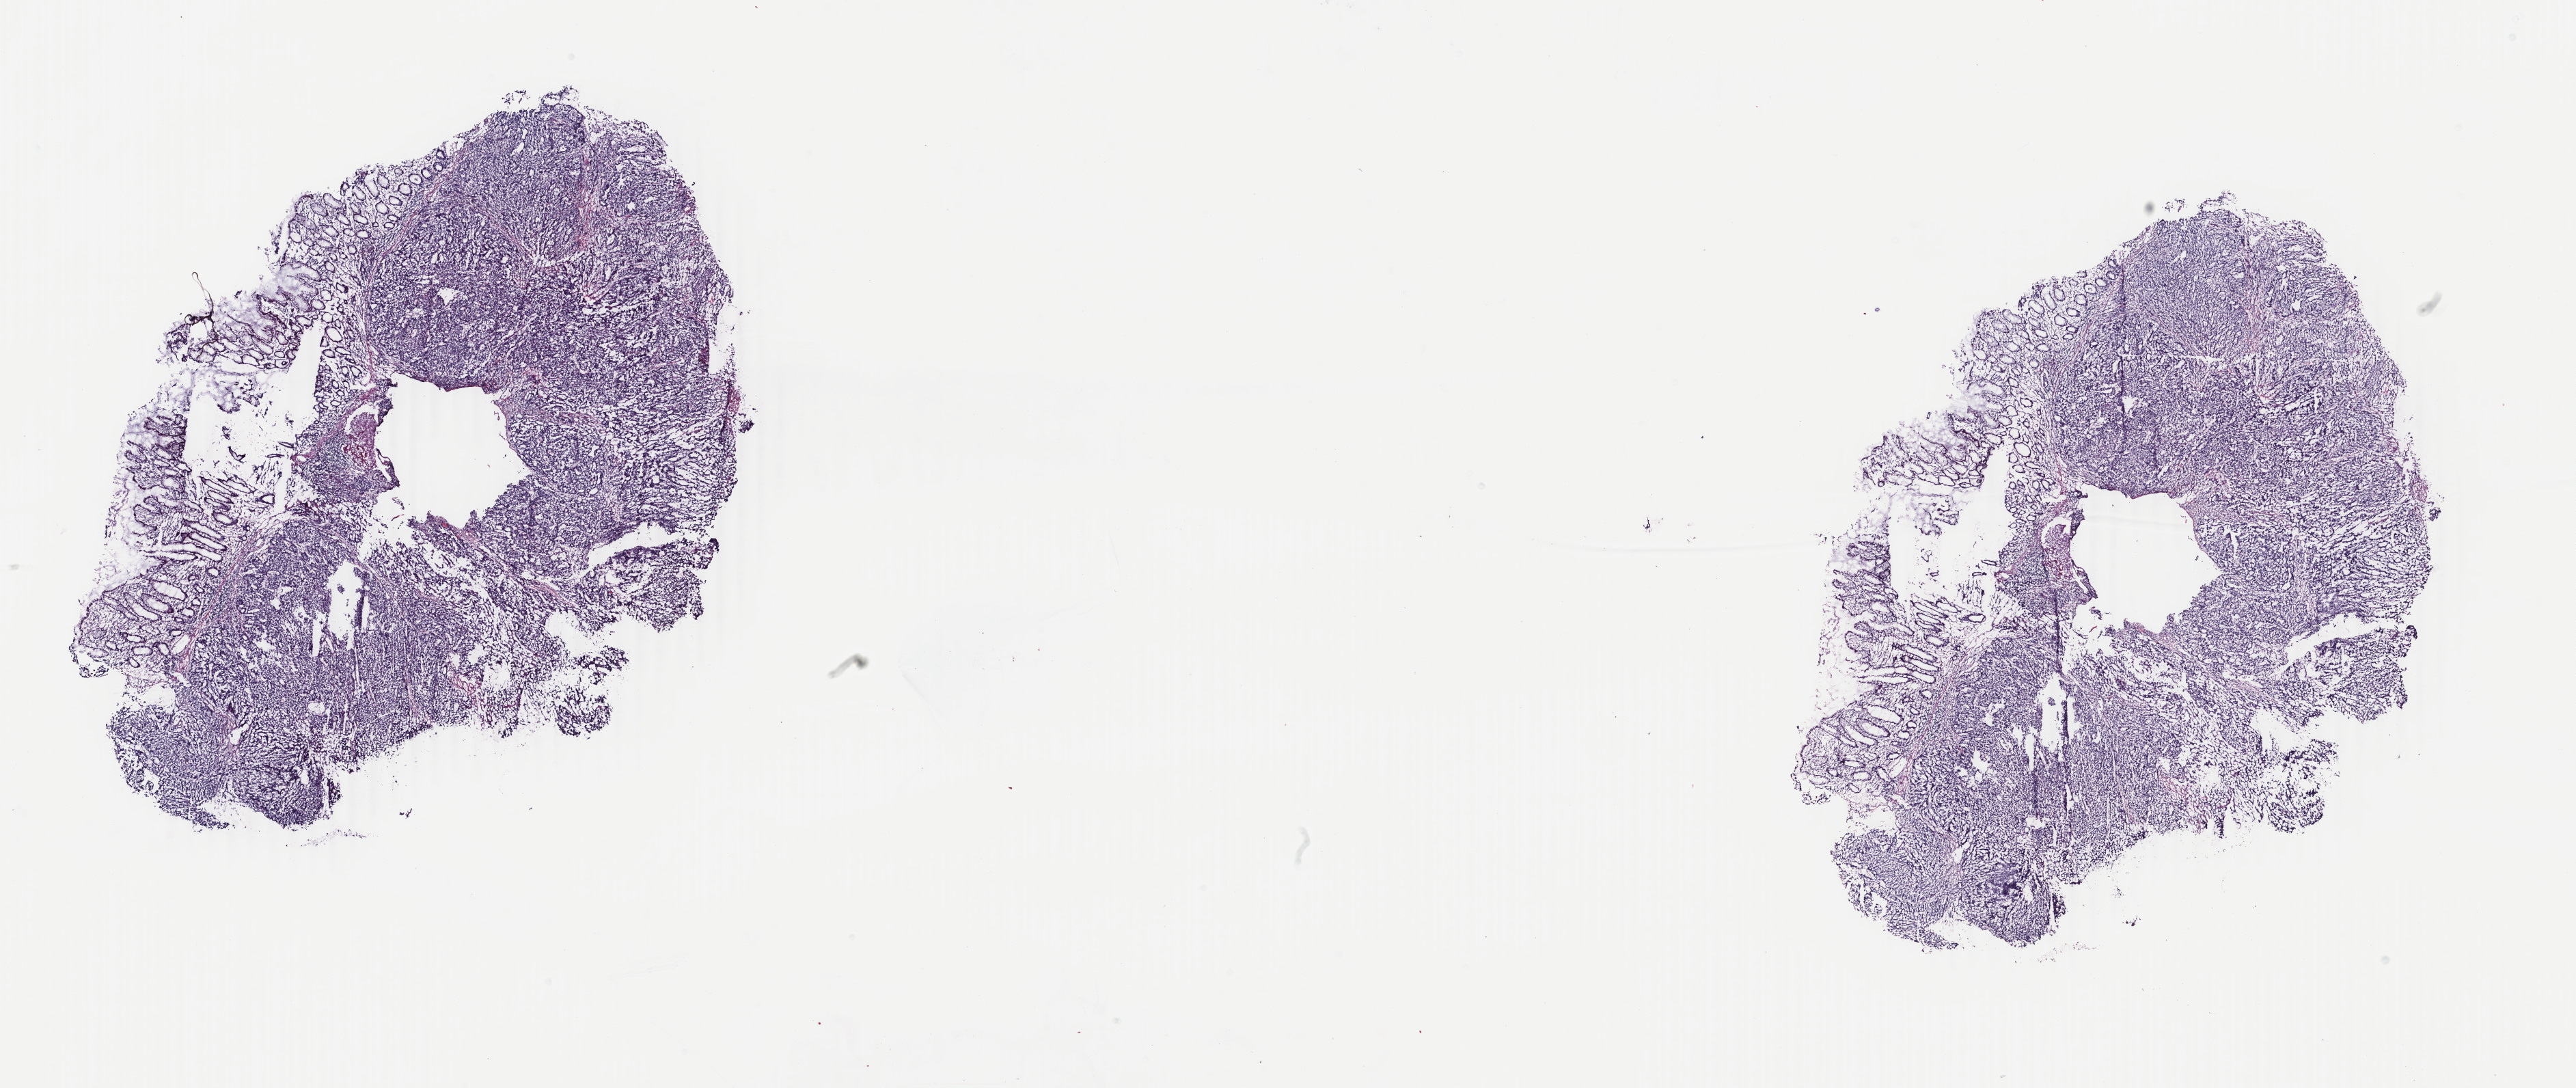
H&E-stained whole-slide image, low-resolution overview of the scanned area, about 30.0 x 12.7 mm. Frozen section from the bottom of the tissue portion. Colon, primary tumour sample. Patient: female, age at initial diagnosis 46 years. Pathologist review of this section (percent, as recorded): tumour cells 75%, tumour nuclei 70%, normal cells 12%, stromal cells 11%, necrosis 2%. Infiltration values recorded for this section: lymphocyte infiltration 15%, monocyte infiltration 1%, neutrophil infiltration 2%.
- pathologic diagnosis: Adenocarcinoma, NOS
- AJCC pathologic stage: IIB
- lymph nodes positive (case pathology): 0 of 45 examined
- TNM: T4 N0 M0